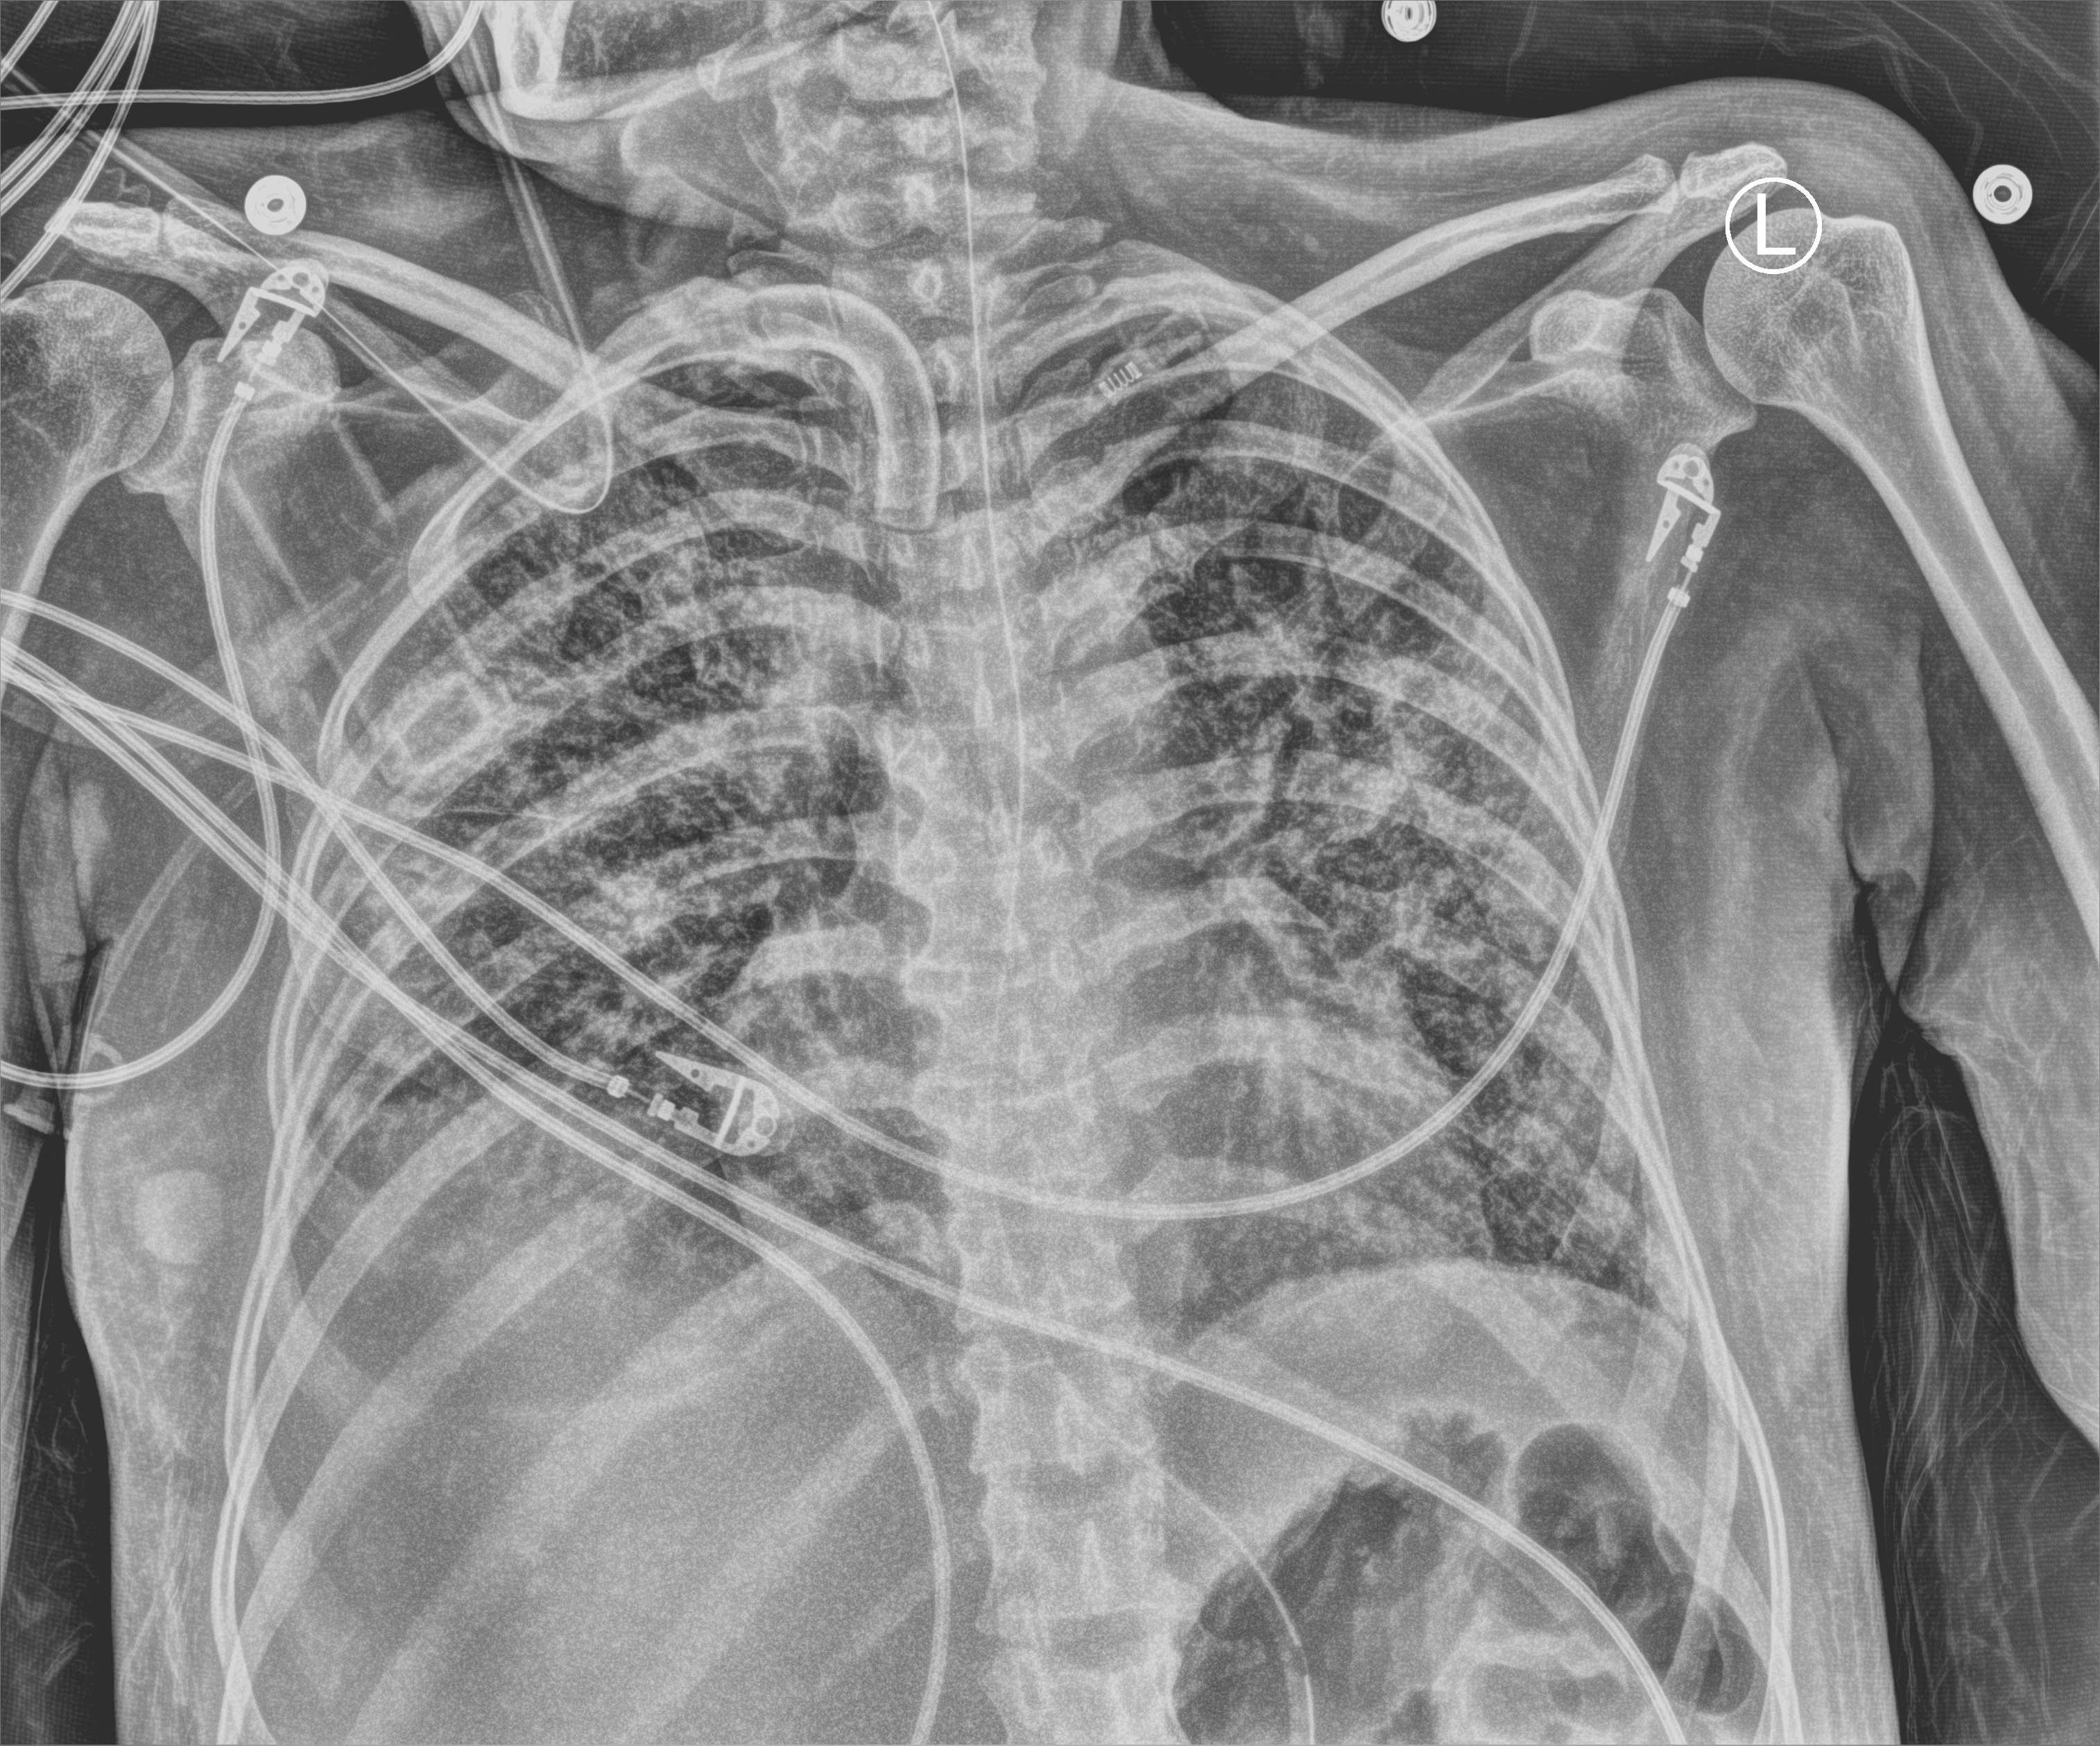
Chest X-ray (portable), anteroposterior (AP) projection. Patient hospitalised with COVID-19; female, aged 18–59 years.
Admission-level facts for this patient (not findings on this image; timing relative to this image not recorded): chronic kidney disease (admission record): no; mechanically ventilated during this hospital stay: yes.